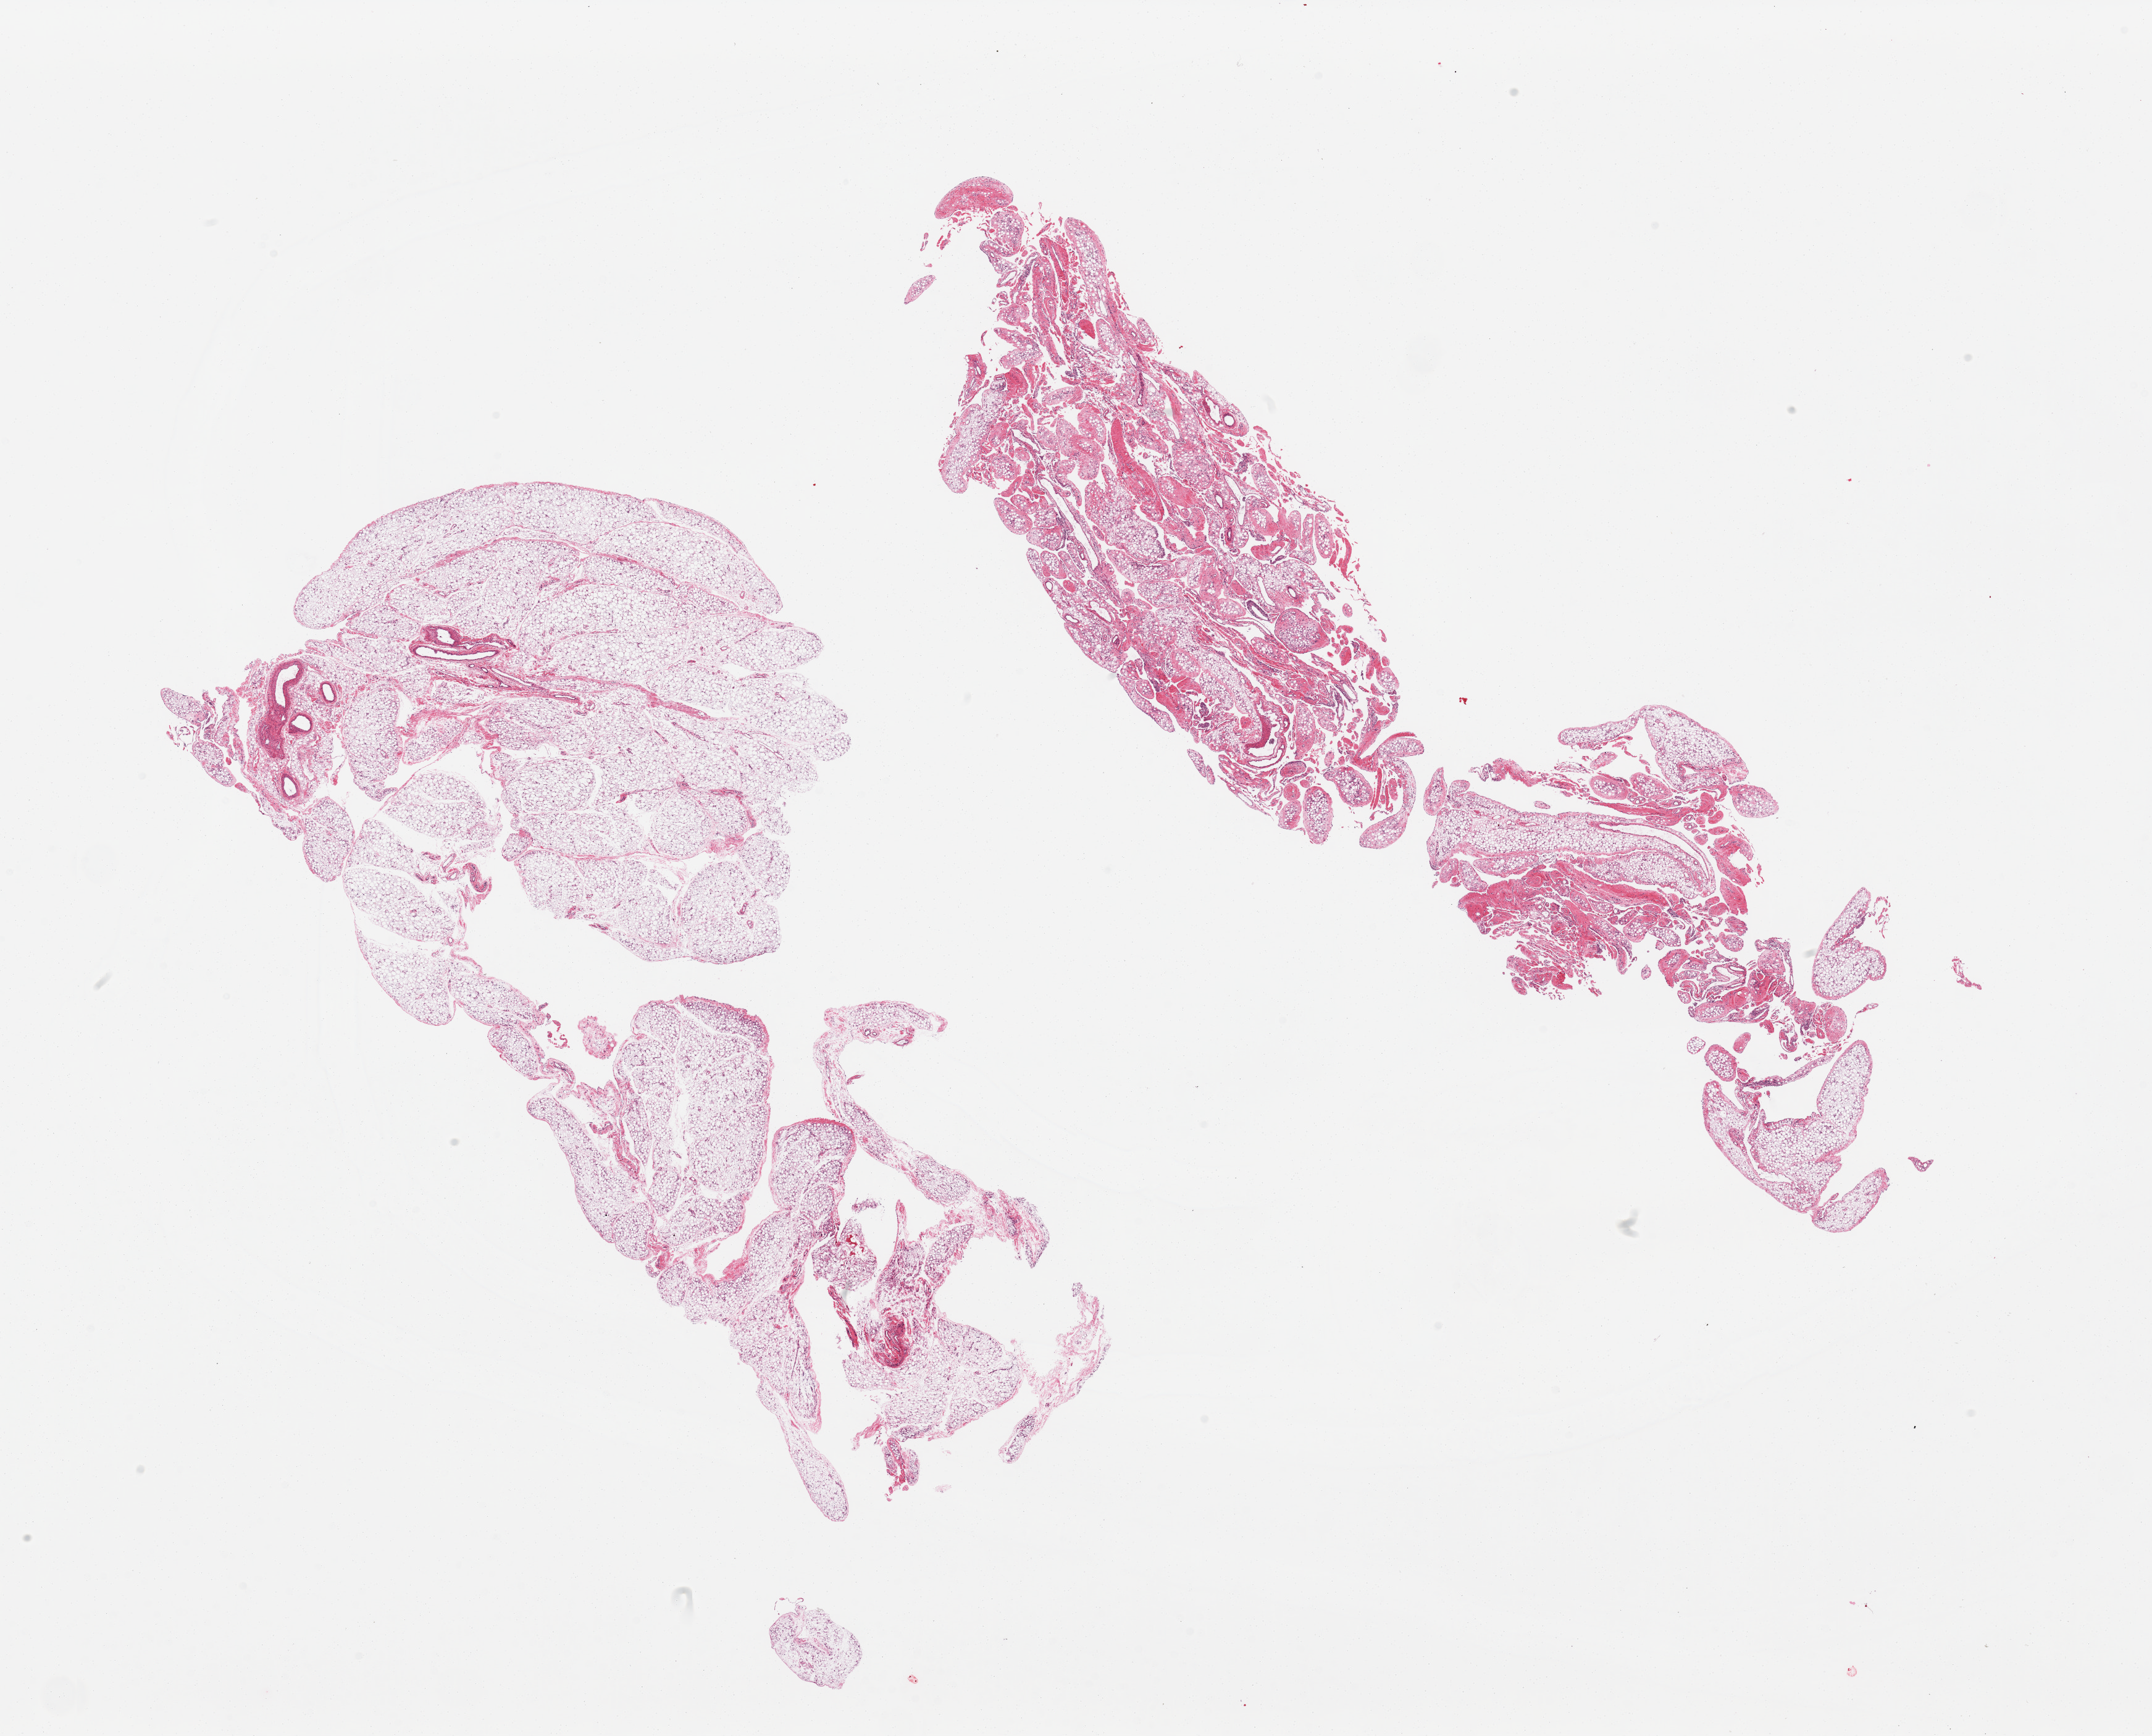
Whole-slide image, hematoxylin and eosin (H&E) stain, low-resolution overview of the scanned area, about 27.6 x 22.2 mm. PAXgene-fixed paraffin-embedded (PFPE) section. Target tissue: omentum. Tissue donor sample. Donor: male.
Review note (as recorded): 2 pieces; 1 fatty, 1 fibrofatty.